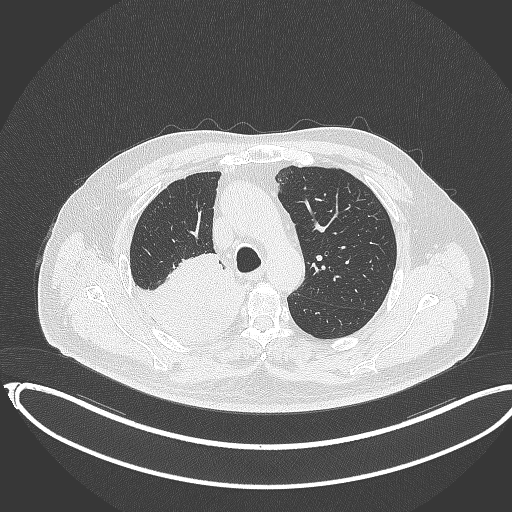
Chest CT, one axial slice. Reconstruction kernel B70f. Lung window (W 1500 / L -600 HU). 1 mm slice thickness. 512 × 512 image matrix, field of view 436 × 436 mm. Male patient, age 68 years. From the clinical record (not read from this slice): clinical TNM (as recorded): T2a N0 M0.
Structures marked on this image (bounding box drawn by a radiologist):
- lung tumour (recorded histology: adenocarcinoma): bounding box [x1, y1, x2, y2] px = [132, 256, 245, 348]